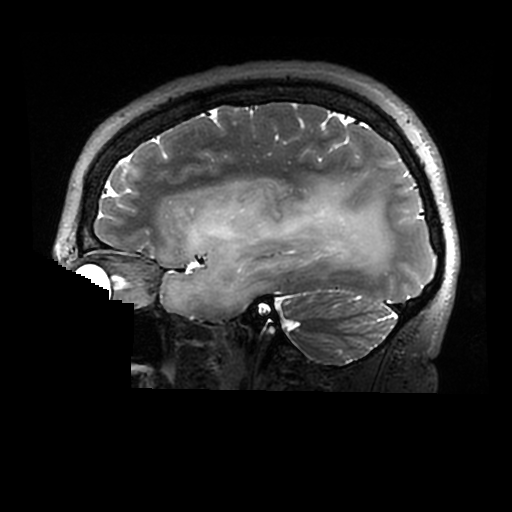
Brain MRI from a brain-tumour surgery series, one sagittal slice. Slice 205 of 320 in the series (ordered by position). 0.6 mm slice thickness. 512 × 512 image matrix, field of view 240 × 240 mm. From the clinical record (not read from this slice): histopathology: Astrocytoma; WHO grade: 2; IDH mutation: yes.
Annotated regions visible in this slice (manually delineated by an expert):
- tumour: box from (x=161, y=180) to (x=391, y=312) px